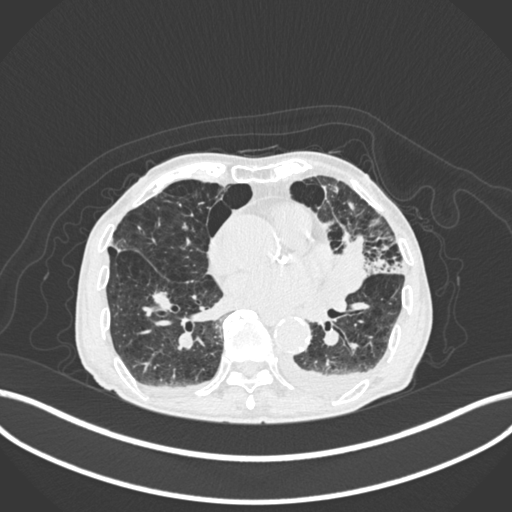
Chest CT, one axial slice. Lung window (W 1500 / L -600 HU). 512 × 512 image matrix. Male patient, age 90 years or older. From the clinical record (not read from this slice): clinical TNM (as recorded): T2b N1 M0.
Structures marked on this image (rectangle marked by the reading radiologist):
- lung tumour (recorded histology: squamous cell carcinoma): bounding box (x1, y1, x2, y2) in pixels: (338, 232, 373, 298)